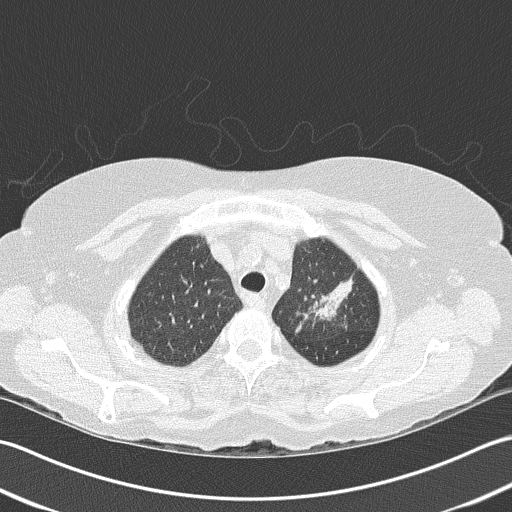
Low-dose screening chest CT, axial slice. Baseline annual screen. Lung window (W 1500 / L -600 HU). Slice 132 of 159 in the series. Female, age 68 years at enrolment.
Lesion marked by an expert reader, bounding box (x1, y1, x2, y2) in pixels: (292, 257, 366, 330). Screening reader's record for this exam: no non-calcified nodule ≥4 mm recorded. Later outcome: lung cancer diagnosed 763 days after this screen (after the third annual screen) — adenocarcinoma, NOS, left upper lobe, poorly differentiated (G3), stage IB (AJCC 6th edition), 50 mm at pathology.